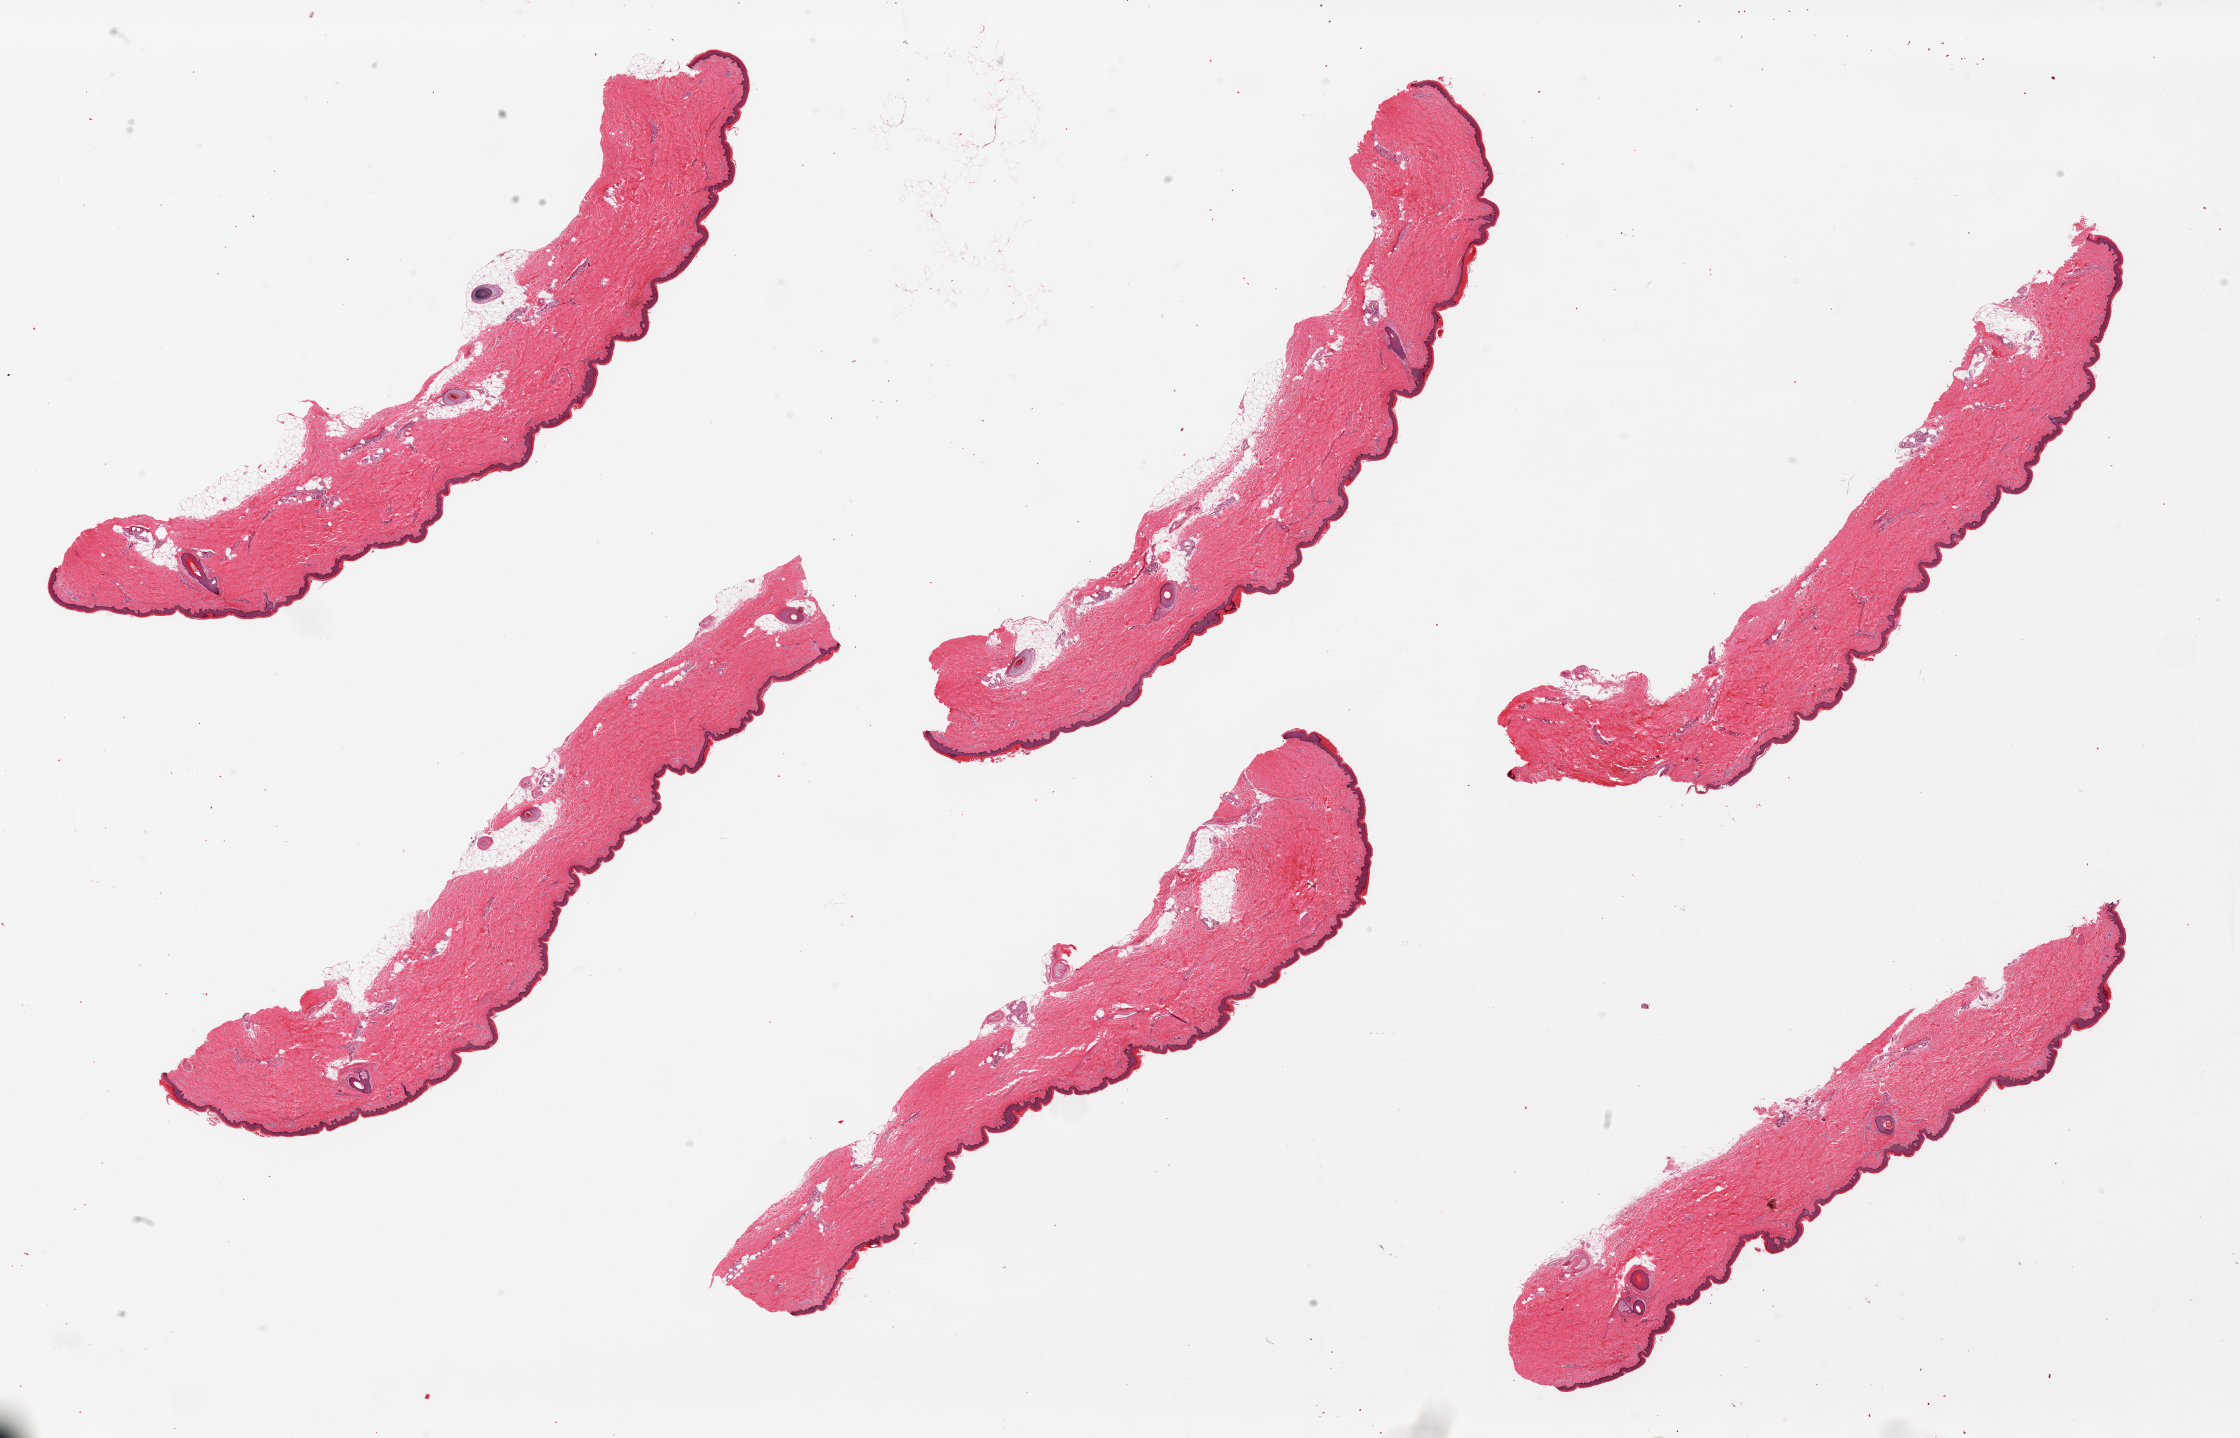
Digitized H&E-stained section — shown as a low-resolution overview of the whole scanned area (about 35.4 x 22.8 mm). PAXgene-fixed, paraffin-embedded tissue. Section of skin of lower leg (target tissue). Donor tissue sample. Donor: male.
Reviewer comment on this tissue sample: 6 pieces, up to 10% attached and internal adipose tissue, squamous epithelium is 50 to 75 microns thick.